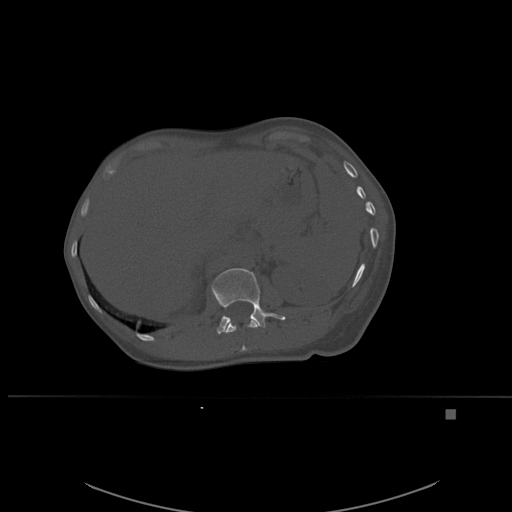
CT including the spine, one axial slice. Slice 267 of 537 in the series (ordered by position). Bone window (W 1800 / L 400 HU). 1.5 mm slice thickness. 512 × 512 image matrix, field of view 440 × 440 mm. Female patient, age 45 years. From the clinical record (not read from this slice): primary cancer: lung.
Annotated regions visible in this slice (semi-automatically segmented with operator editing):
- L1 vertebra: bounding box <212,268,286,334> (left, top, right, bottom; pixels)
- T12 vertebra: <225,319,260,352>